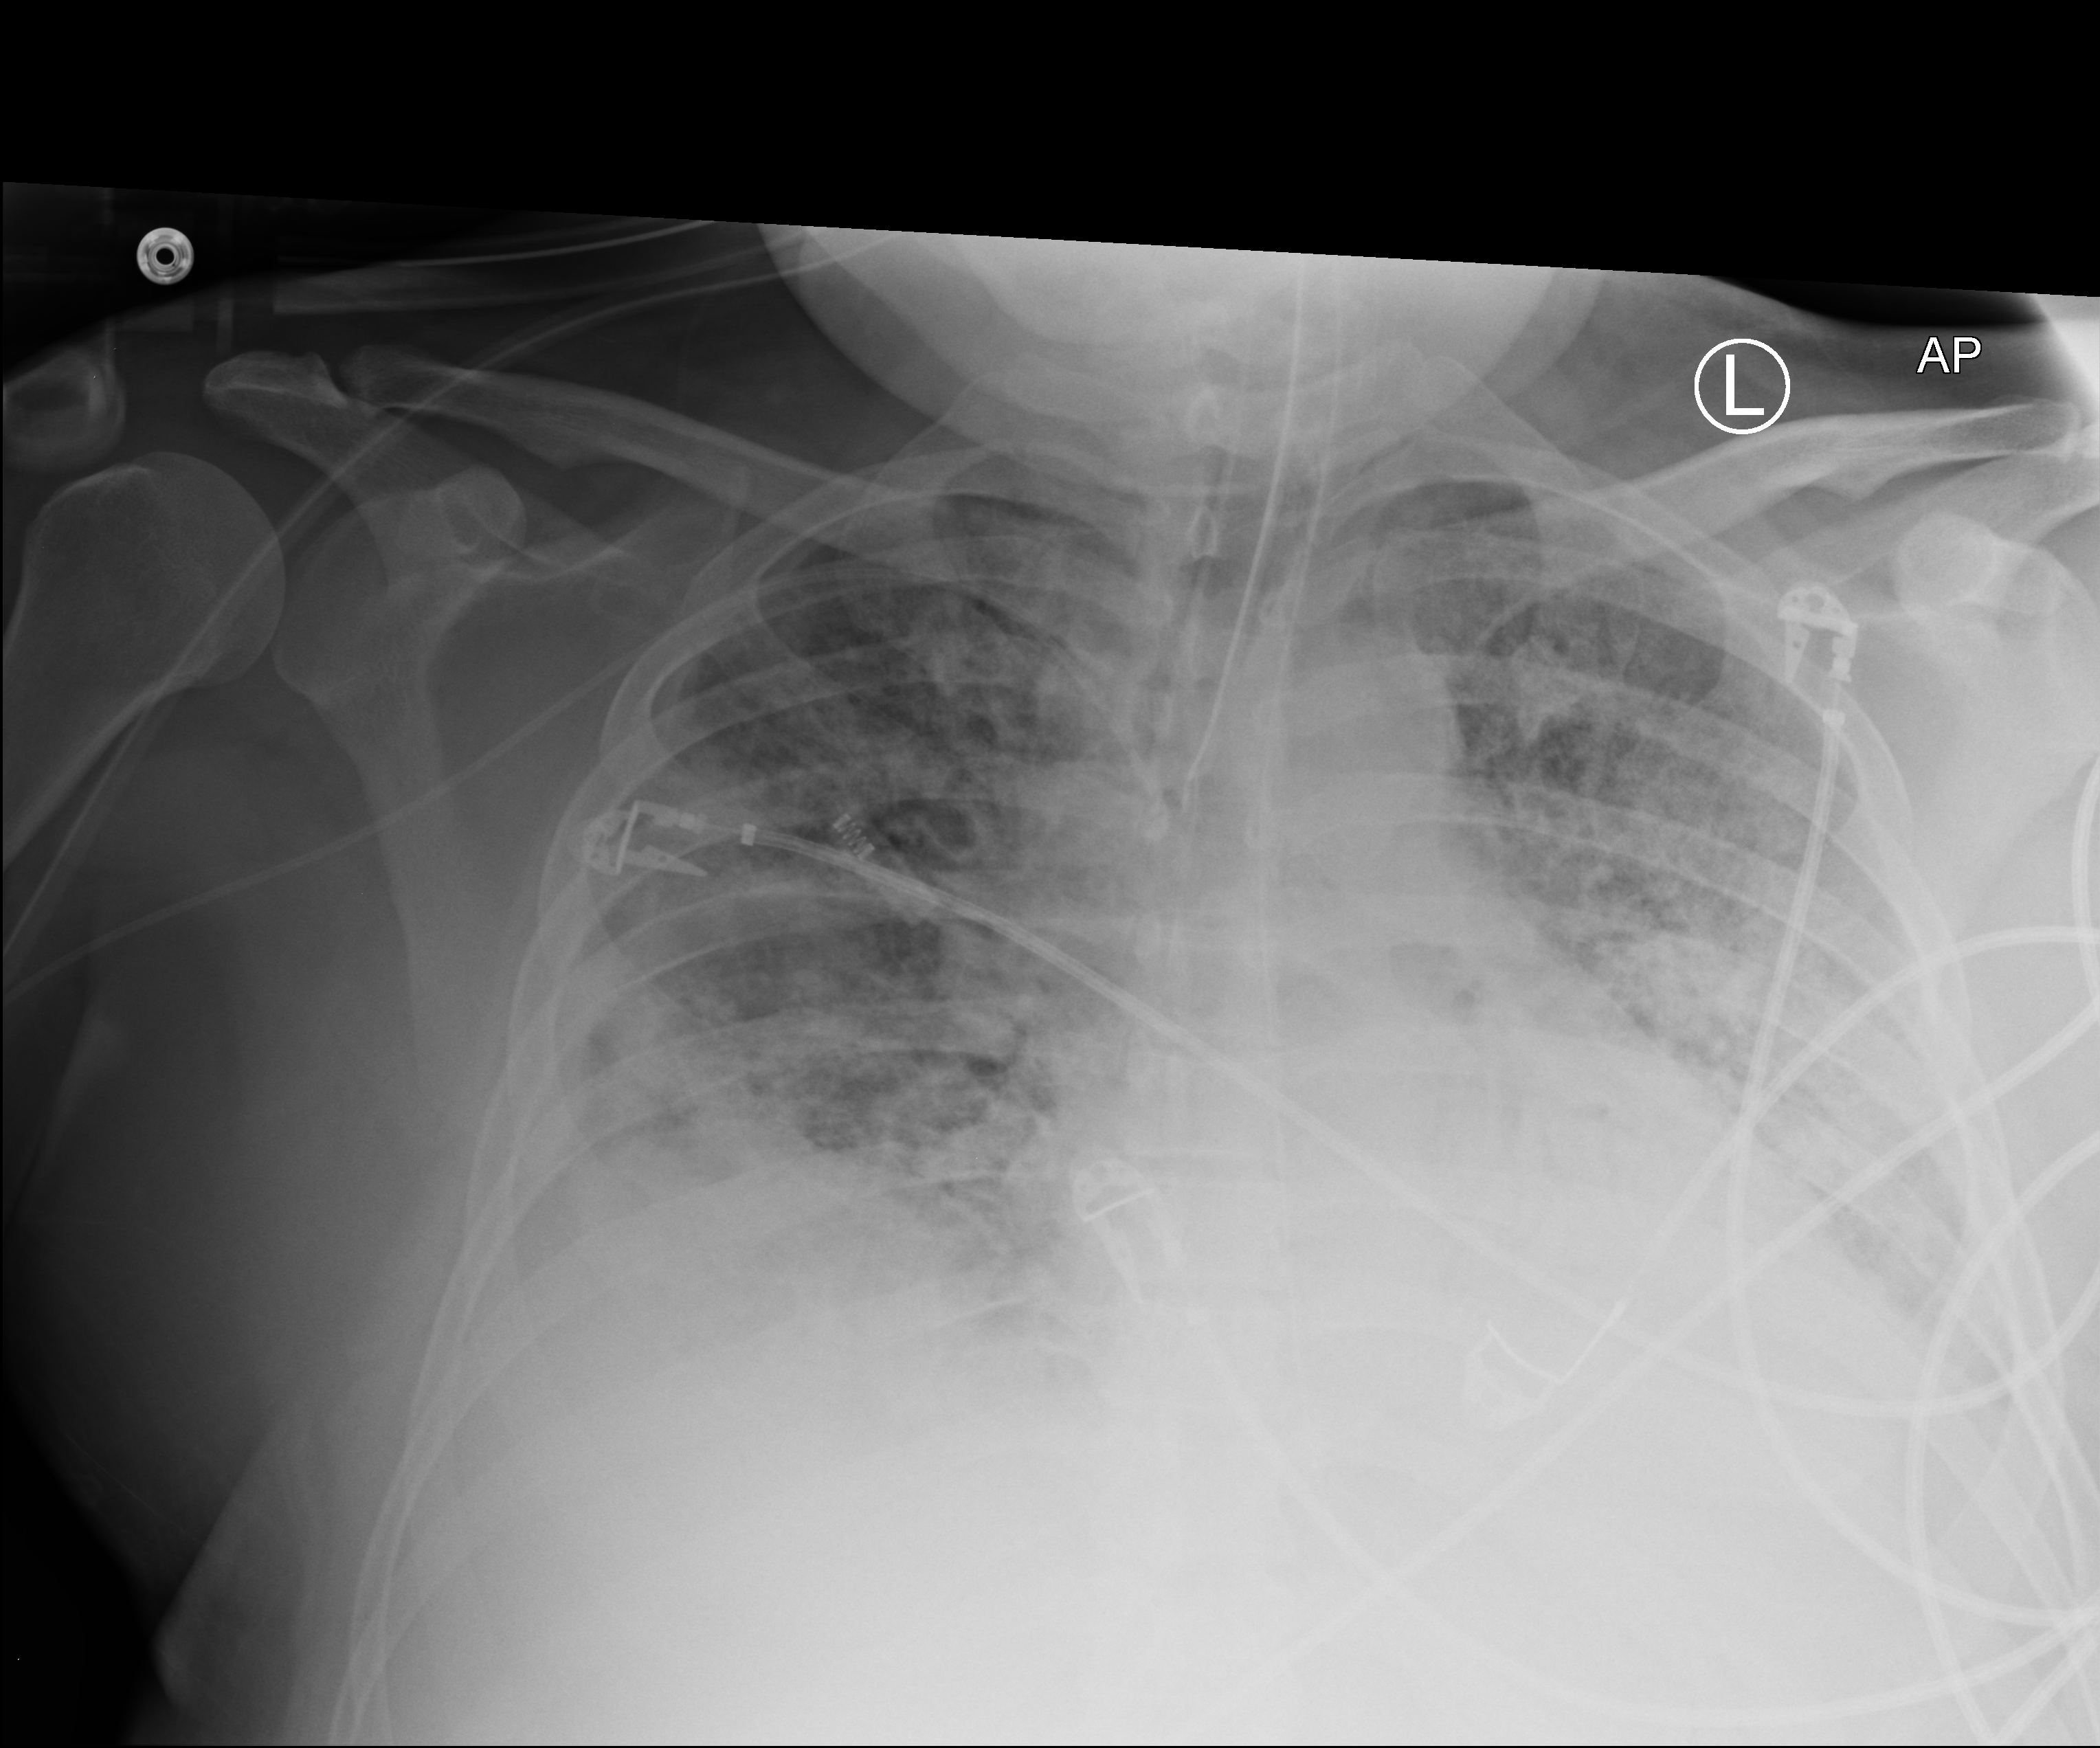
Chest X-ray (portable); anteroposterior (AP) projection. Patient hospitalised with COVID-19; male, aged 18–59 years.
Hospital-stay facts (about this admission, not read from this image; timing relative to this image not recorded):
- COPD (admission record): no
- chronic kidney disease (admission record): no